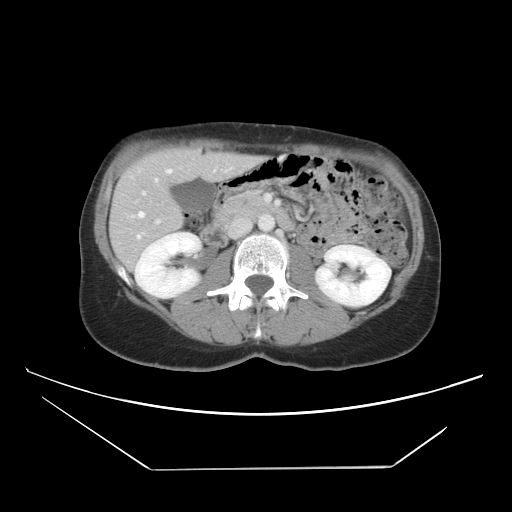
Contrast-enhanced abdominal CT, one axial slice. Intravenous contrast given. Soft-tissue window (W 400 / L 40 HU). 5 mm slice thickness. 512 × 512 image matrix. Female patient, age 52 years. Case-level facts recorded for this patient, not image findings: diagnosis: colorectal cancer liver metastases, imaged before liver resection; multiple liver metastases: yes; largest metastasis: 5.5 cm; disease in both lobes: yes.
Structures marked on this image (manually delineated by an expert):
- hepatic veins: bounding box (x1, y1, x2, y2) in pixels: (129, 168, 231, 240)
- liver: (111, 148, 255, 267)
- planned liver remnant (the part of the liver to remain after resection): (116, 148, 214, 210)
- portal vein (with intrahepatic branches): (142, 163, 270, 224)